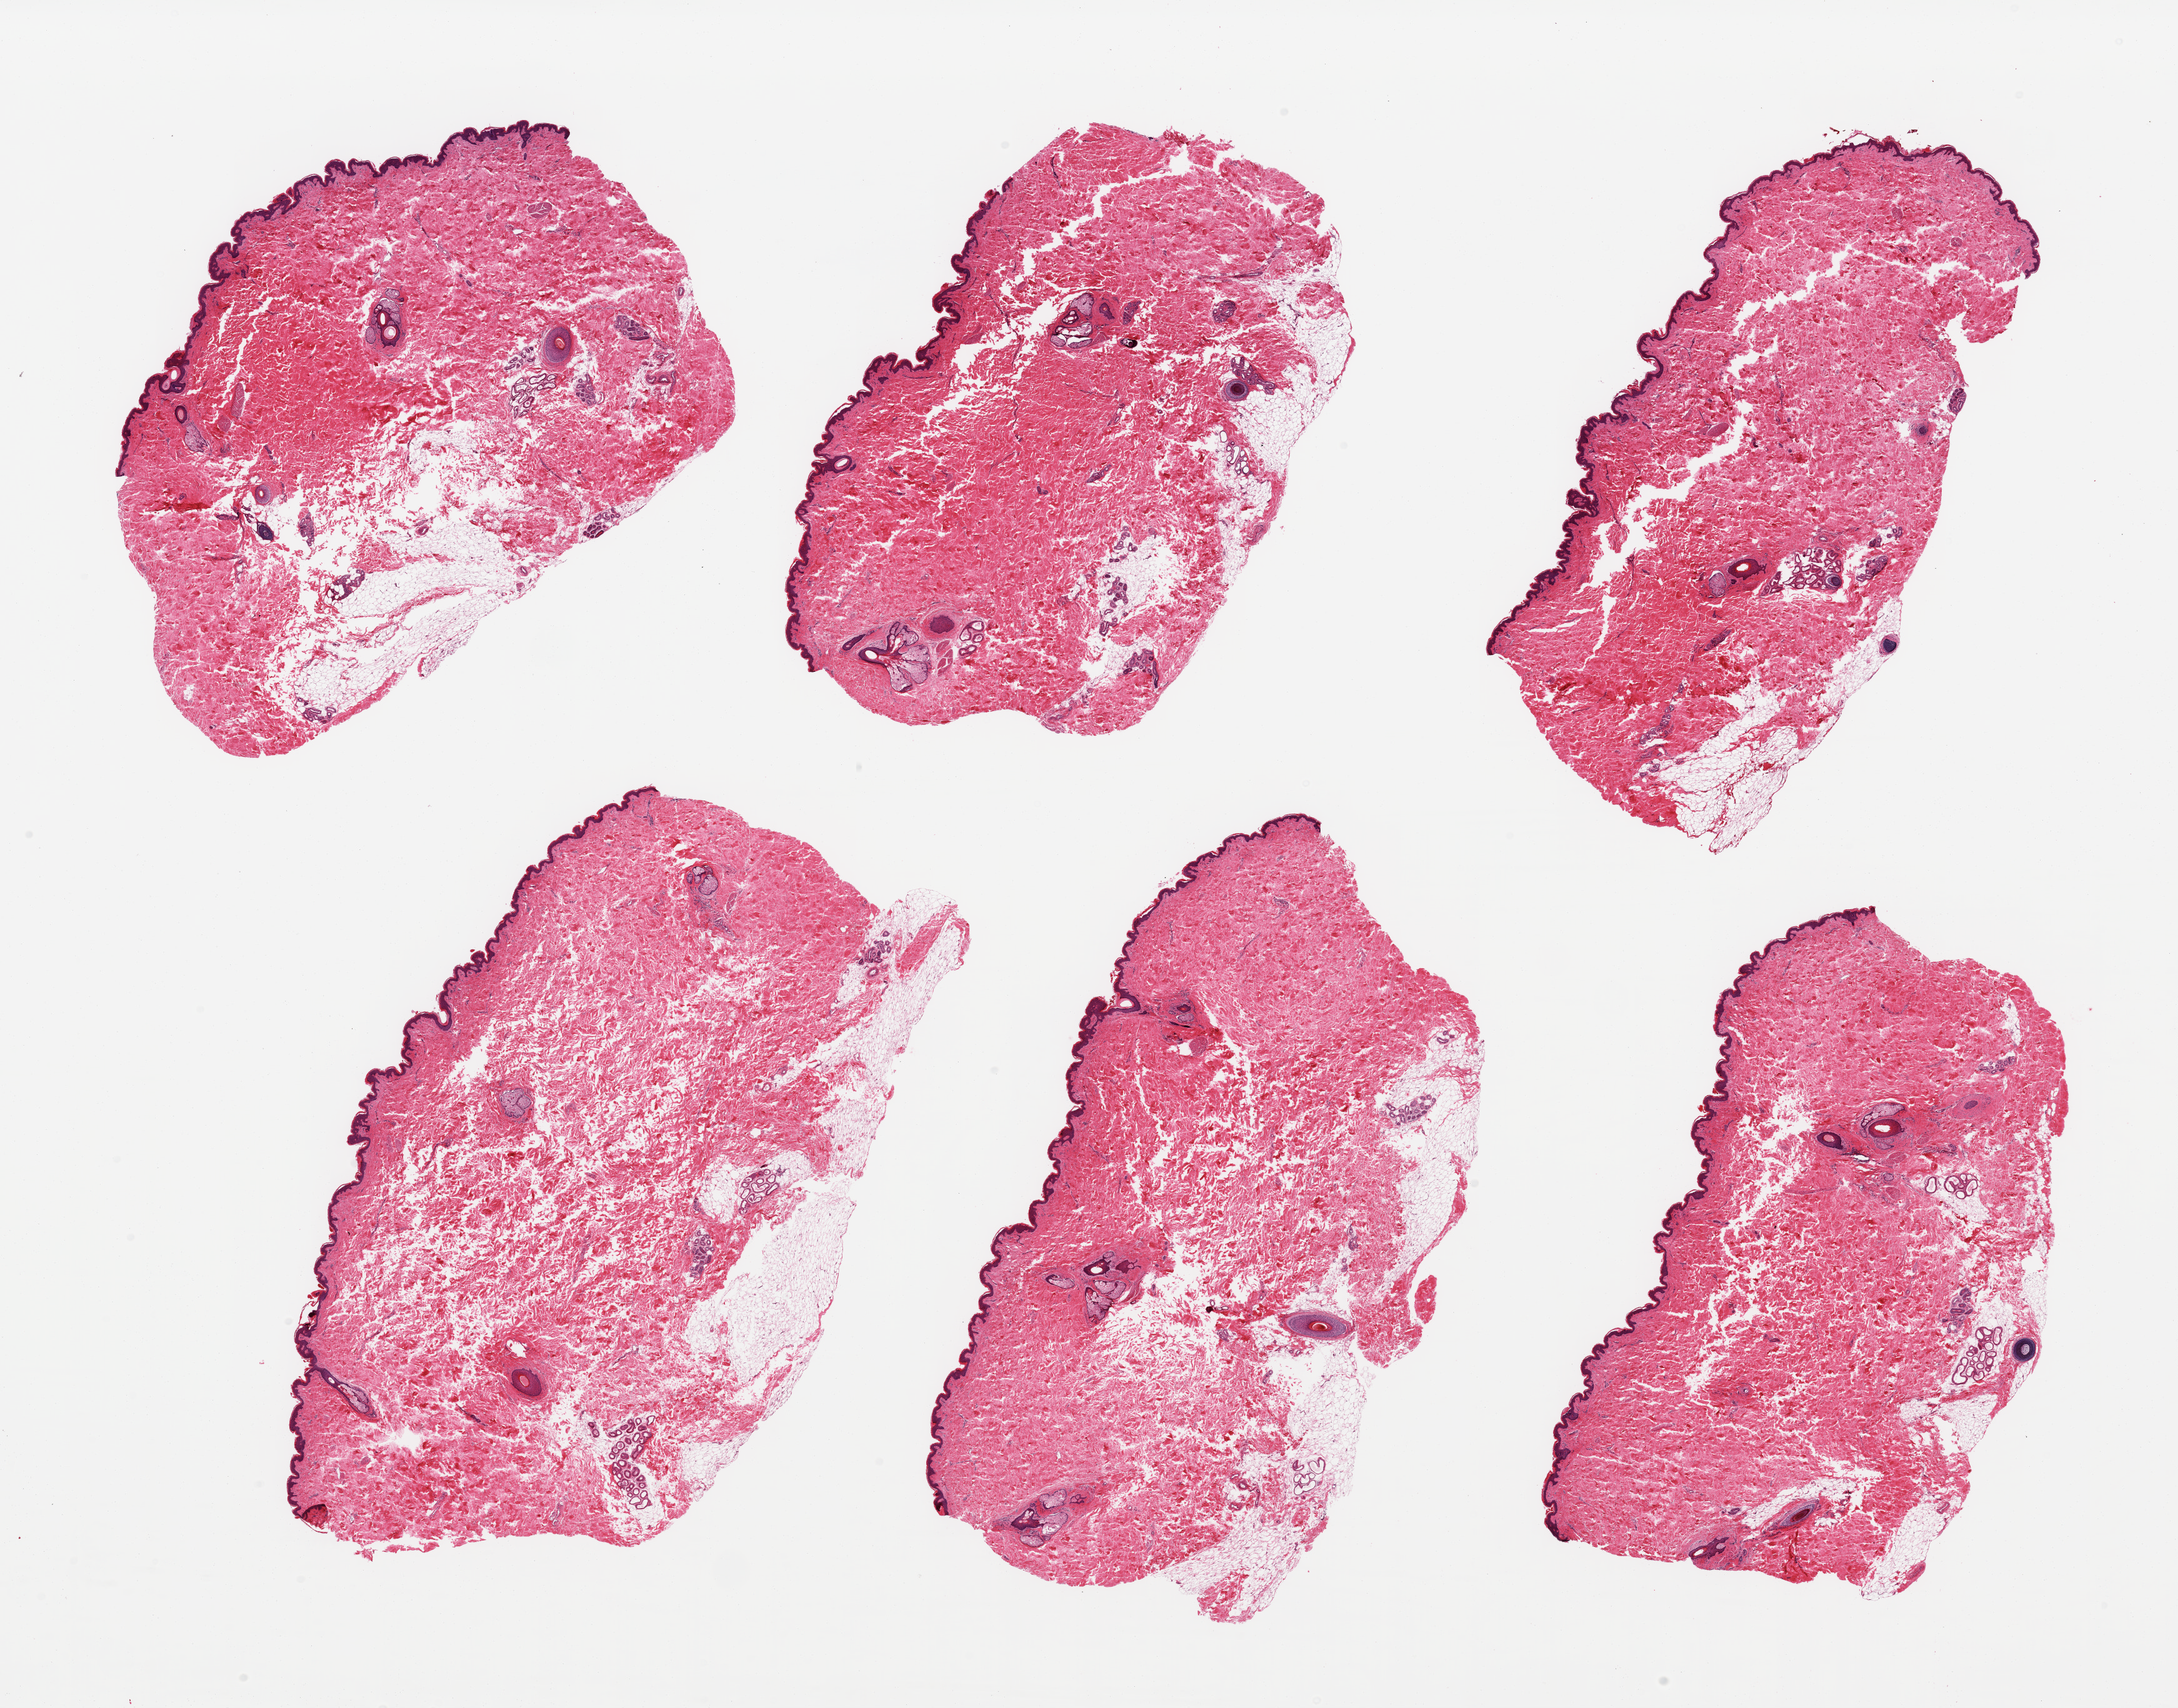
Digitized haematoxylin and eosin-stained section, low-resolution overview of the scanned area, about 27.6 x 21.6 mm. PAXgene-fixed, paraffin-embedded tissue. Section of skin of suprapubic region (target tissue). Tissue donor sample. Male donor.
Pathologist's review note for this sample: 6 pieces, moderate dermal fat; squamous epithelium is ~50-60 microns.